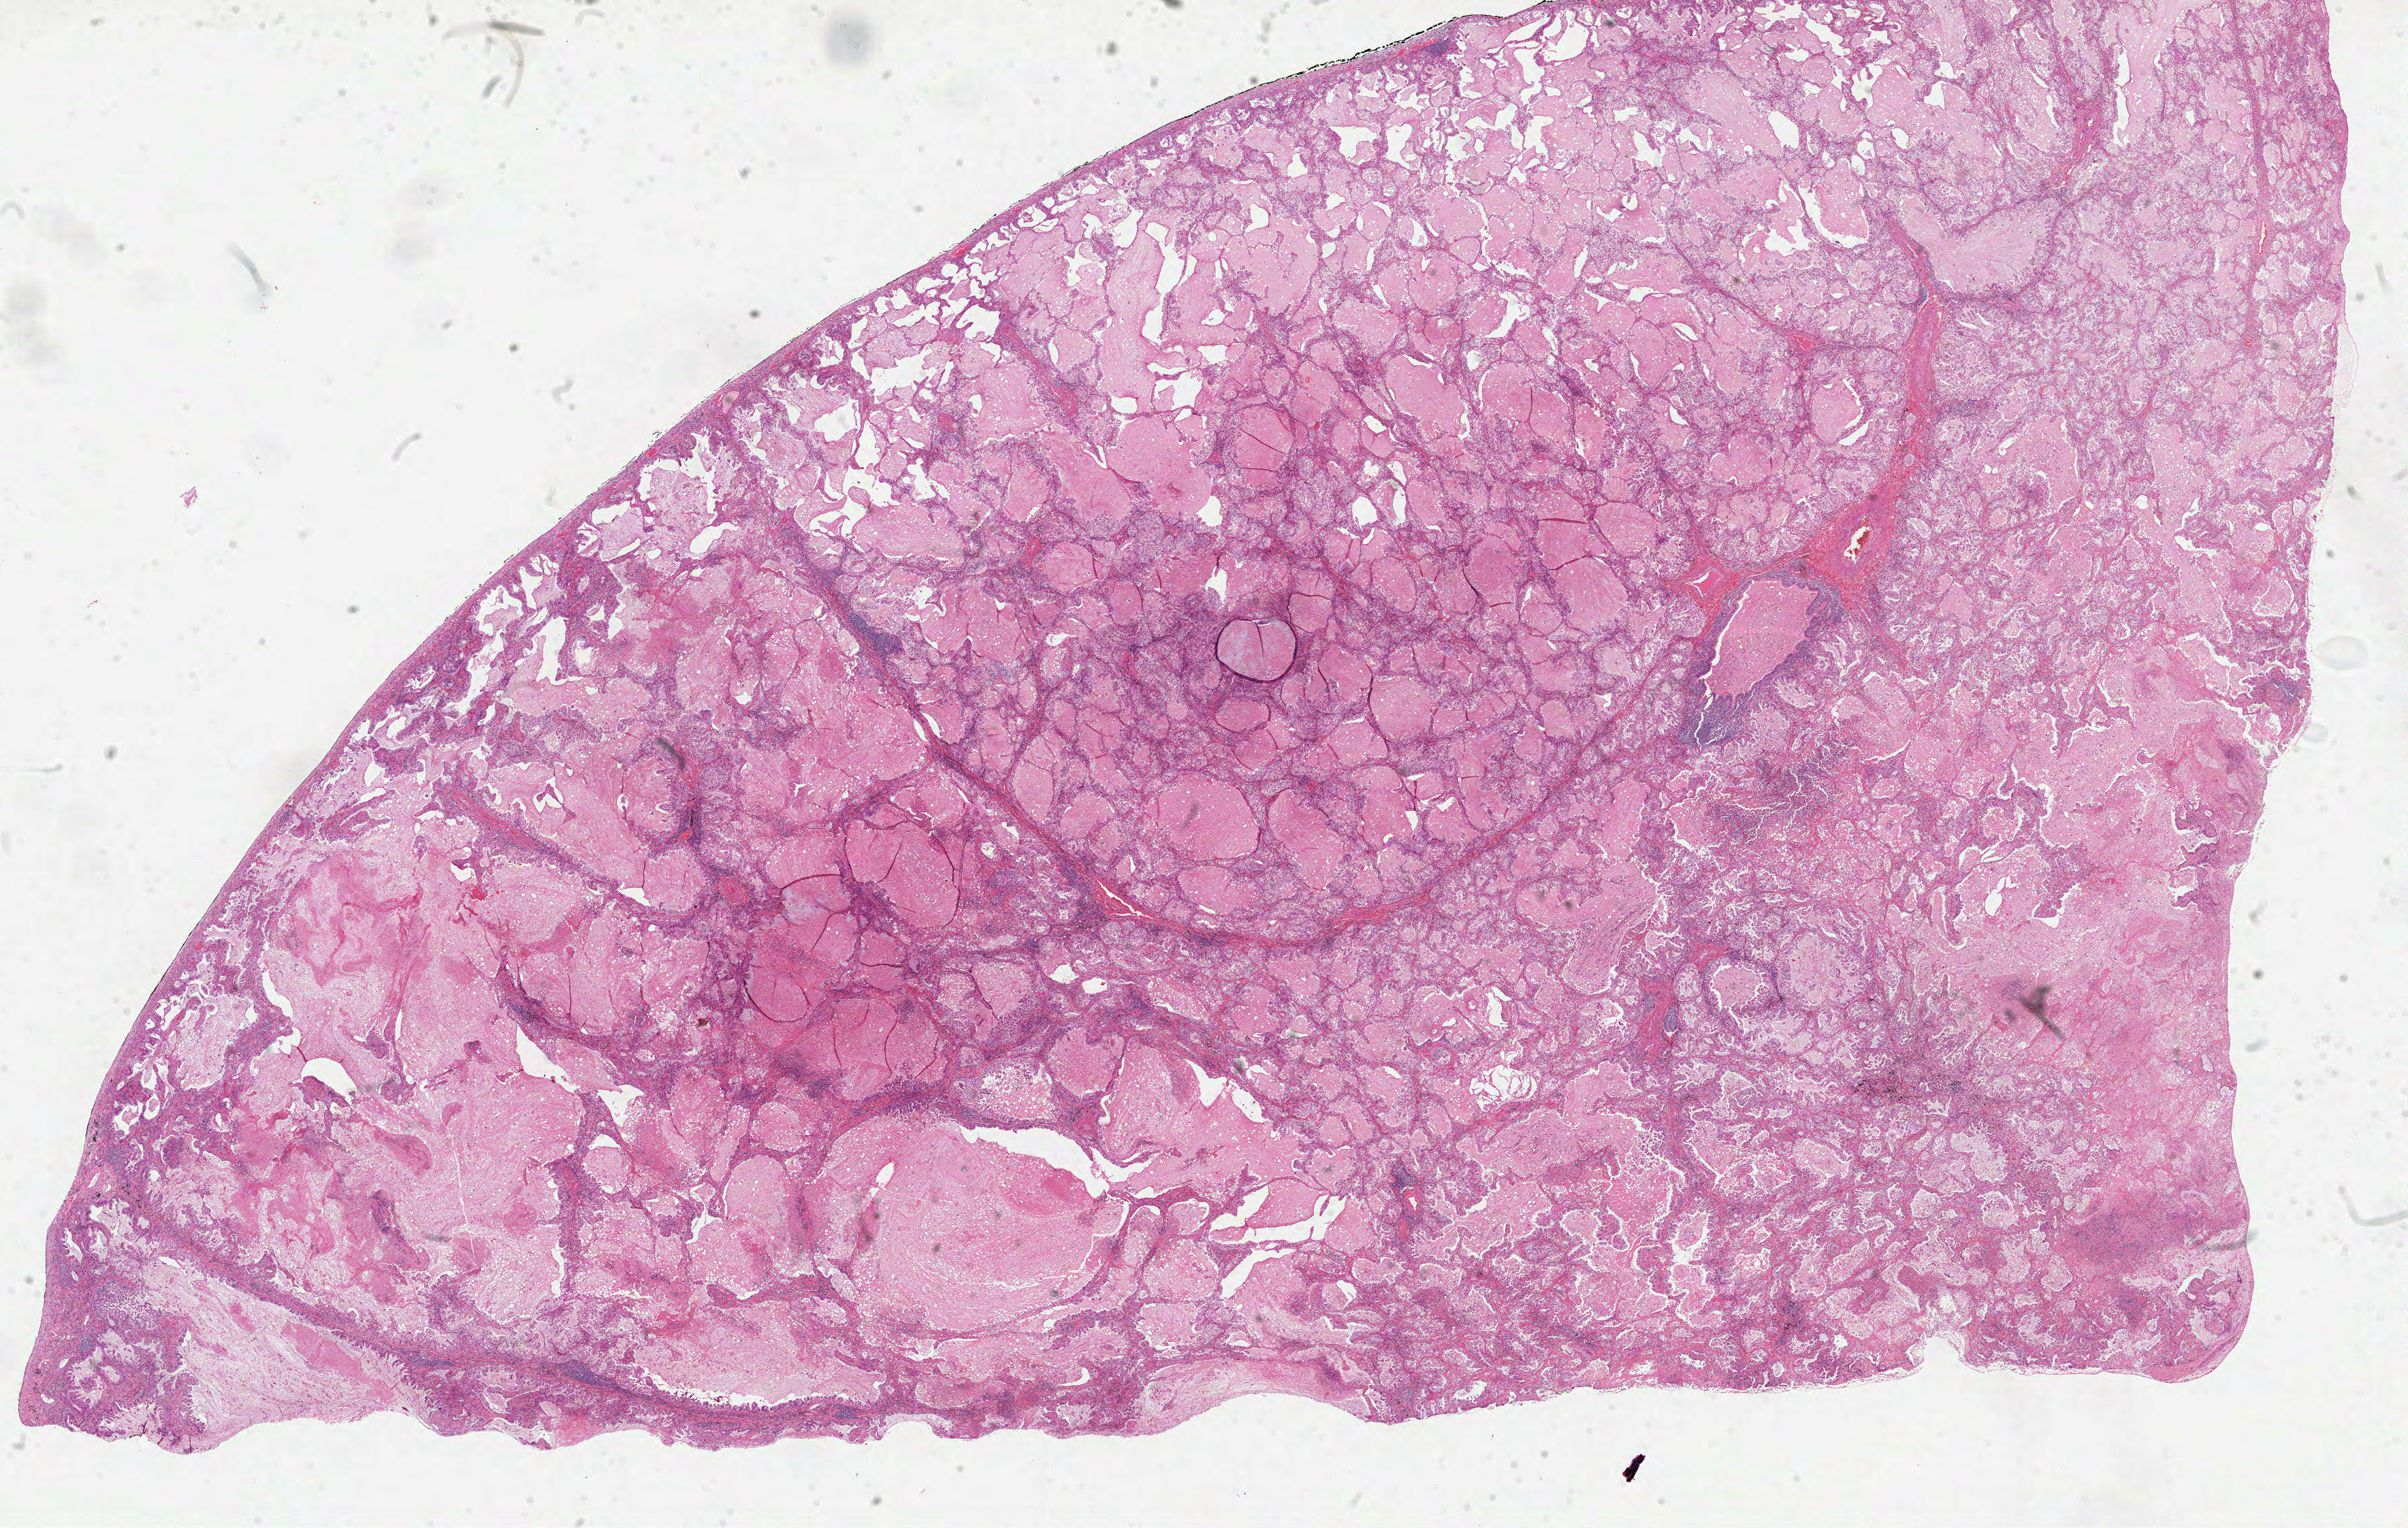
Whole-slide histology image, H&E — whole scanned area (about 28.5 x 18.1 mm, slide scanned at 40x) shown as a low-resolution overview; formalin-fixed paraffin-embedded (FFPE) diagnostic section; primary tumour sample from the lung. Patient: male, age at initial diagnosis 84 years.
Pathologic diagnosis: Adenocarcinoma, NOS (lower lobe, lung).